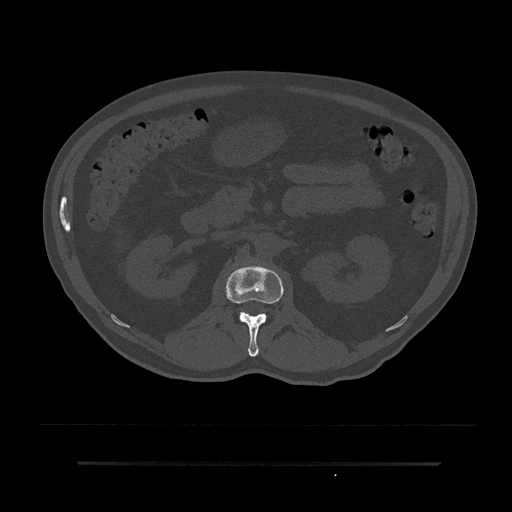
CT including the spine, one axial slice; slice 124 of 797 in the series (ordered by position); reconstruction kernel Br40s/3; 120 kVp; bone window (W 1800 / L 400 HU); 0.5 mm slice thickness; 512 × 512 image matrix, field of view 464 × 464 mm. Patient: male, 59 years. From the clinical record (not read from this slice): primary cancer: bile ducts.
Structures marked on this image (semi-automatically segmented with operator editing):
- L1 vertebra: box from (x=224, y=265) to (x=284, y=357) px